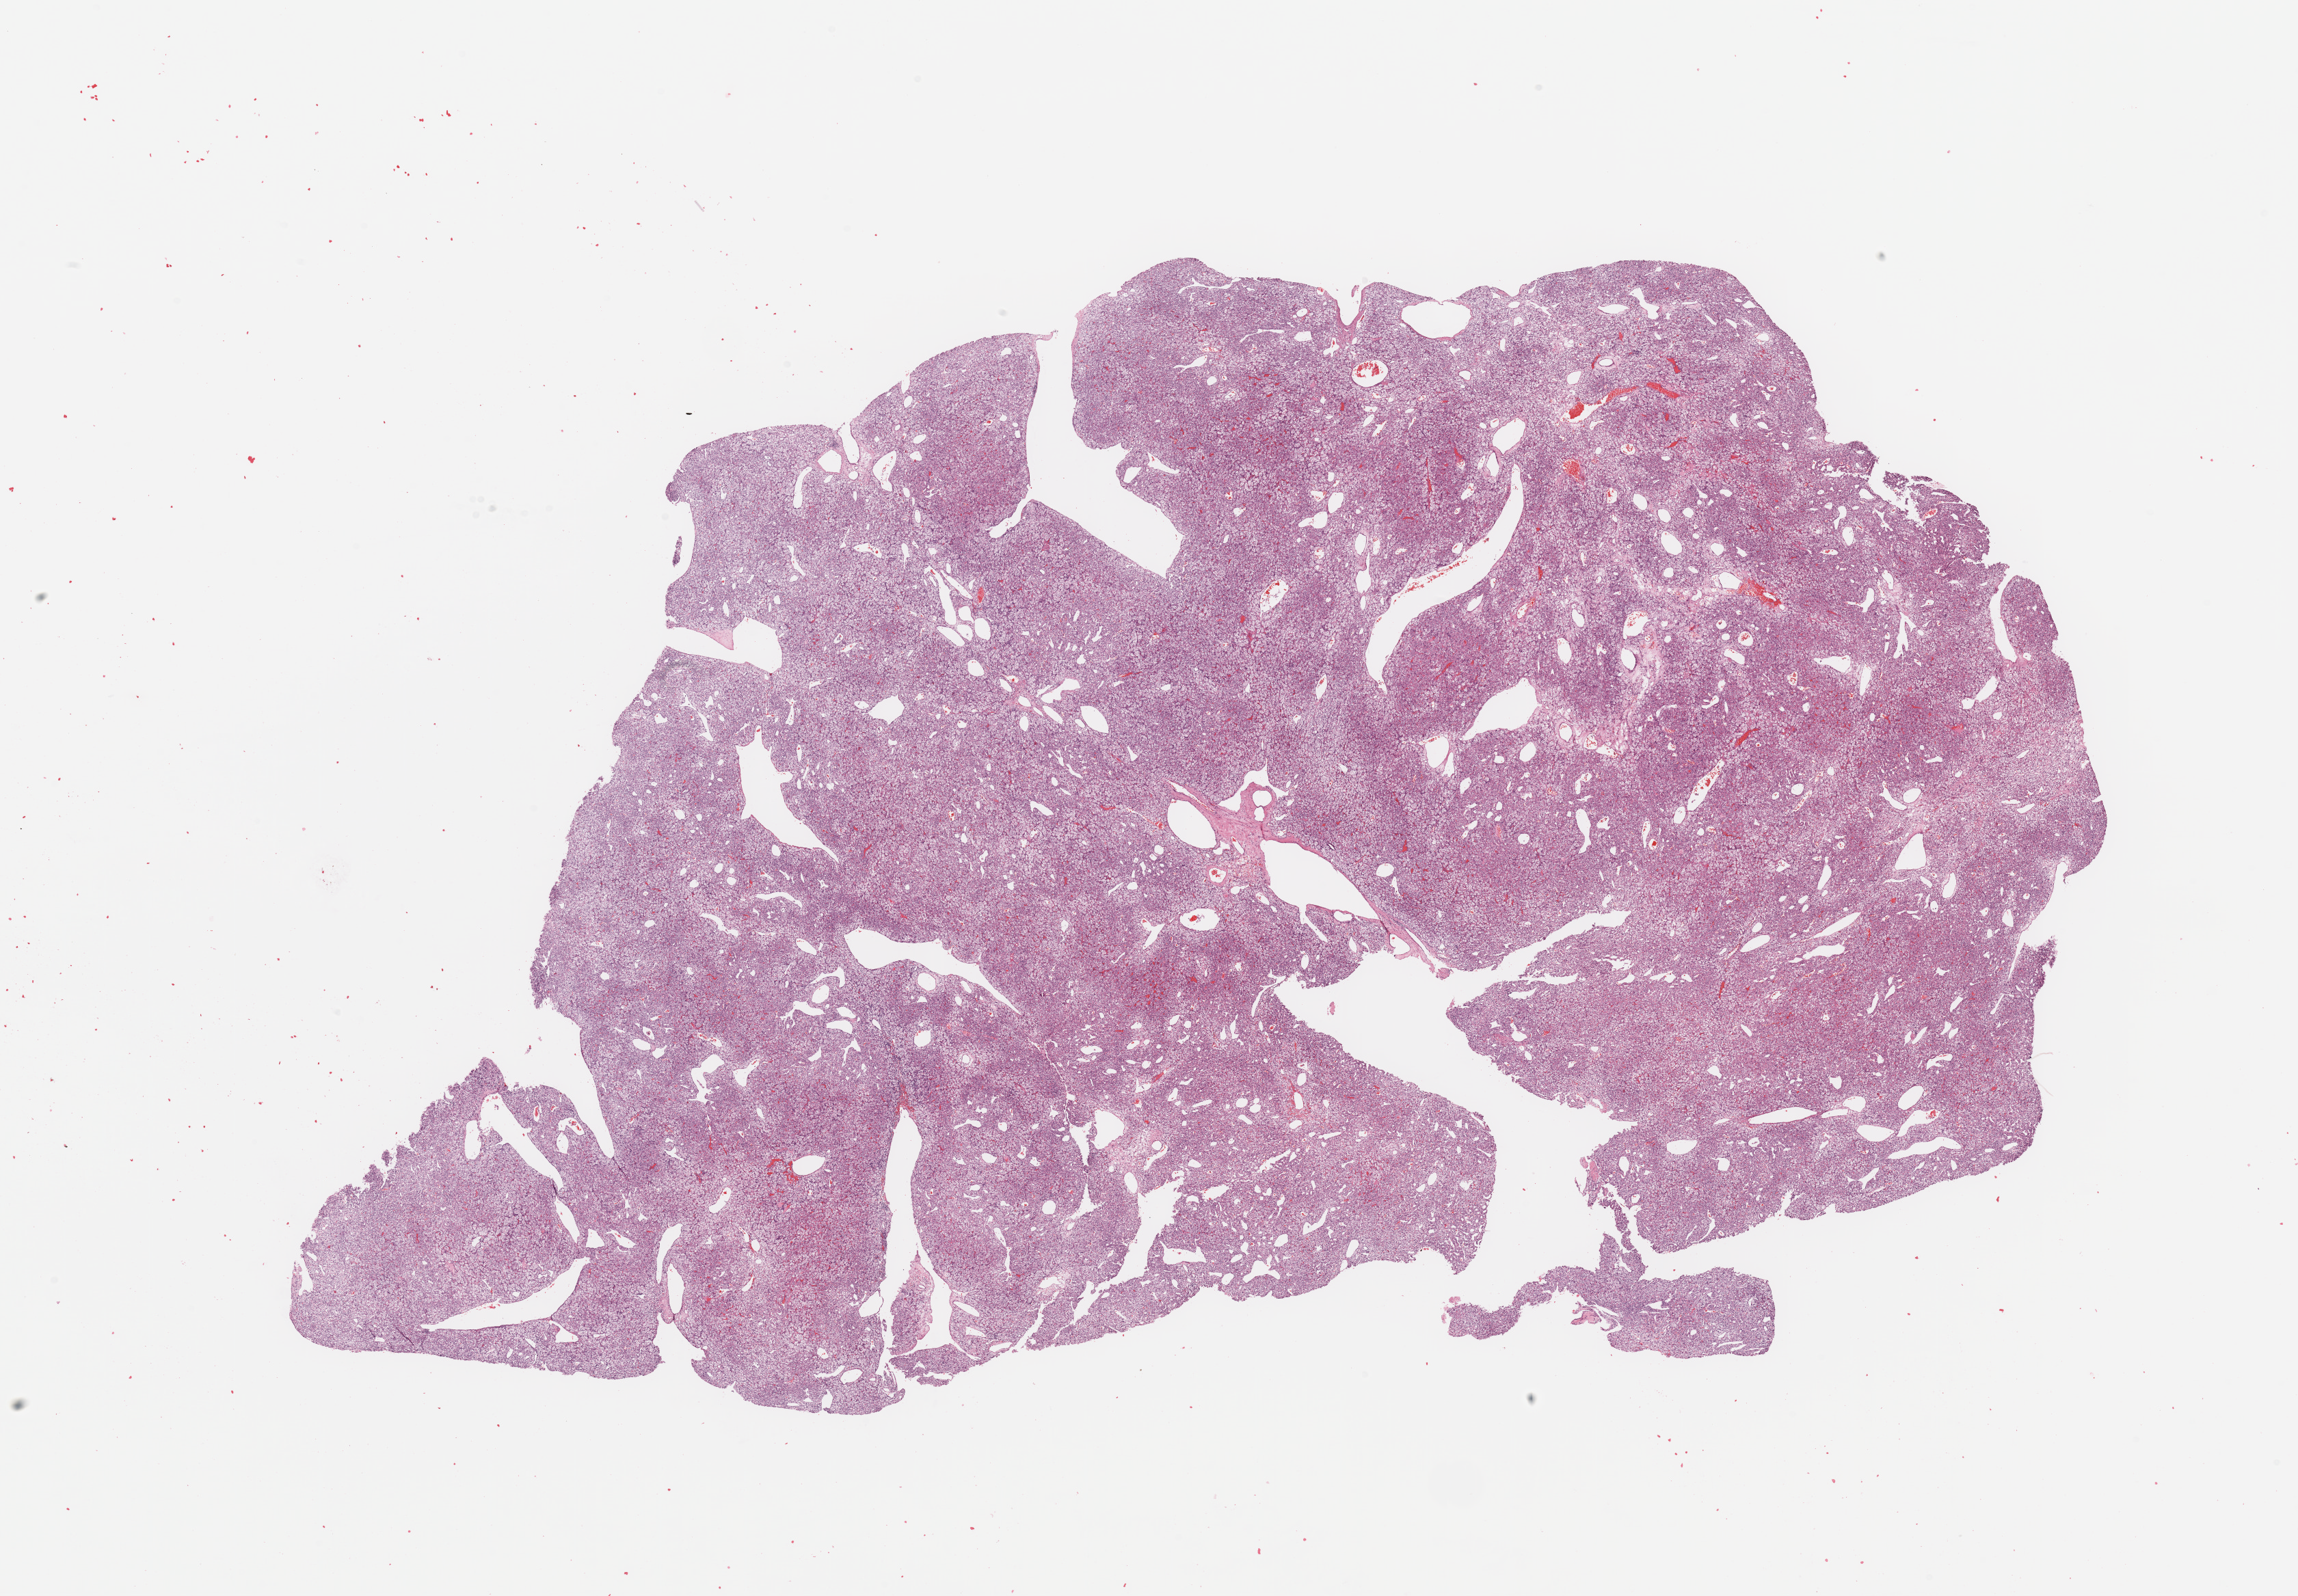
Digitized Hematoxylin and eosin (H&E) stained tissue section (whole slide), low-resolution overview of the scanned area, about 26.6 x 18.5 mm (from a 20x scan), tumour tissue sample, sampled site: kidney. Patient: female, age 76 years. Histologic grade: G2 (moderately differentiated). Composition of this section per pathologist review: tumour nuclei 95%, necrosis 0%.
Diagnosis: Renal cell carcinoma, NOS.